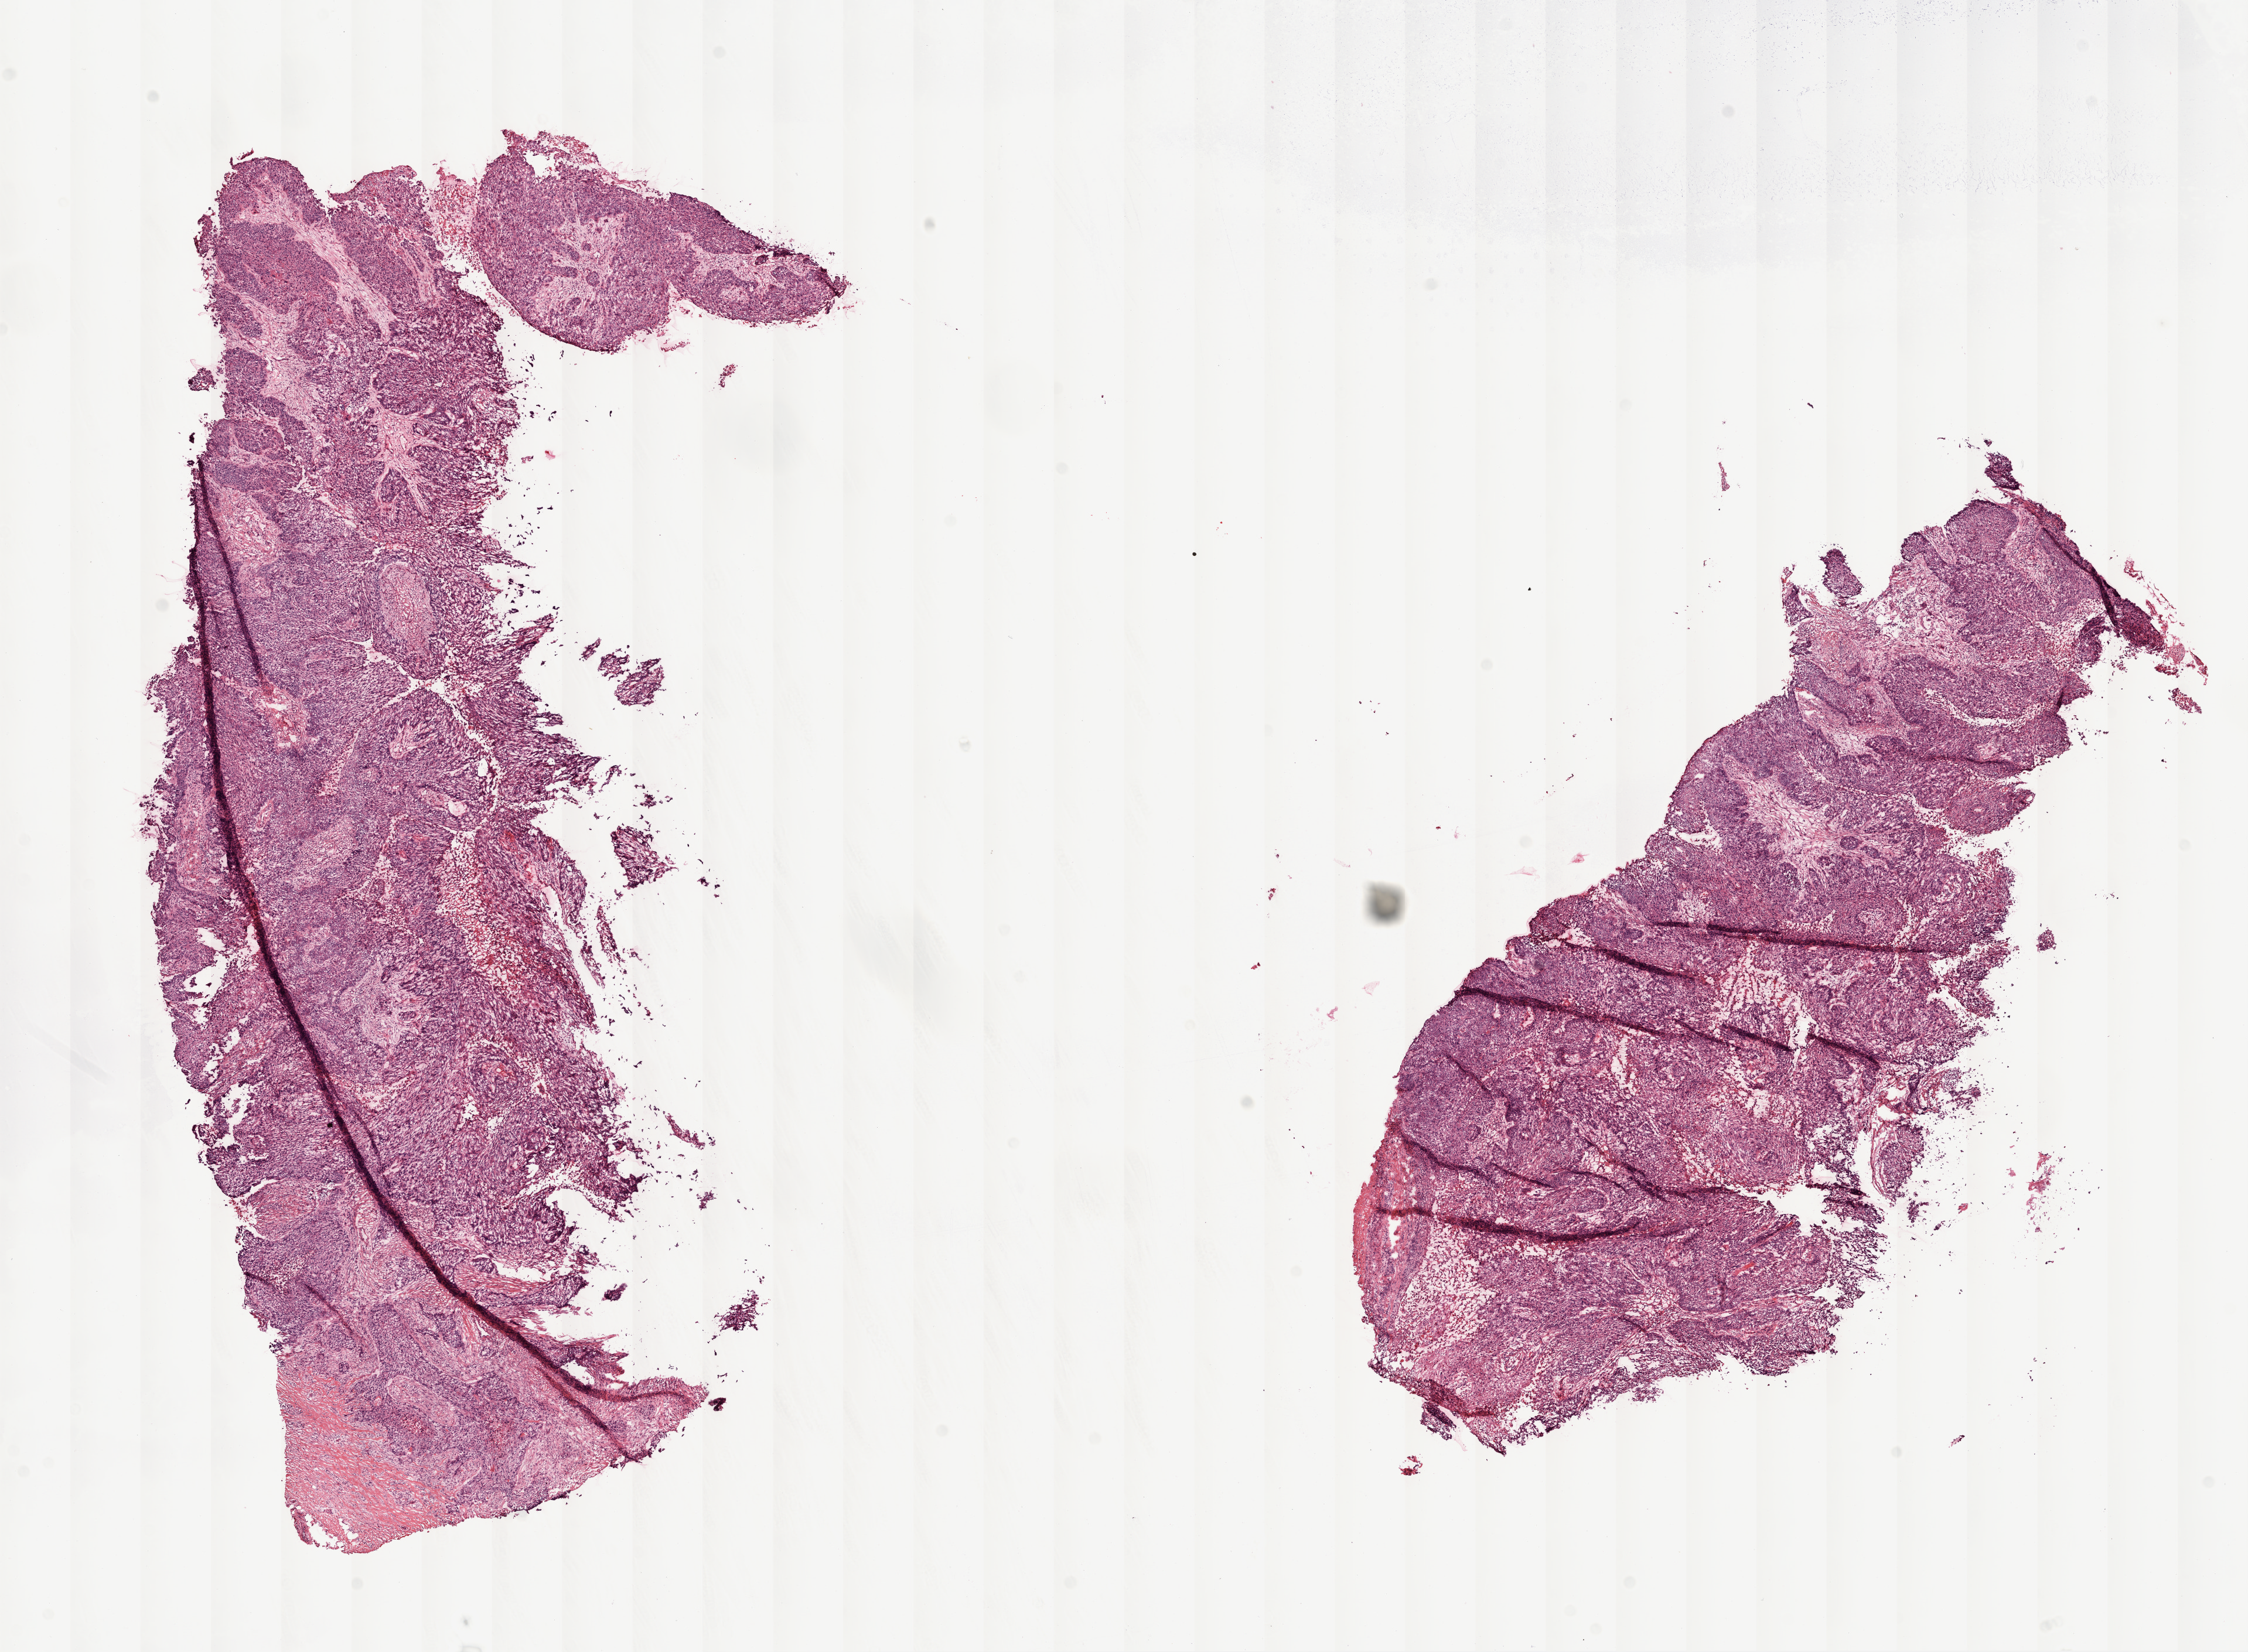
Digitized H&E tissue section (whole slide), low-resolution overview of the scanned area, about 15.5 x 11.4 mm, frozen section, primary tumour sample from the lung. Patient: male, age at initial diagnosis 75 years.
Pathologic diagnosis: Squamous cell carcinoma, NOS.